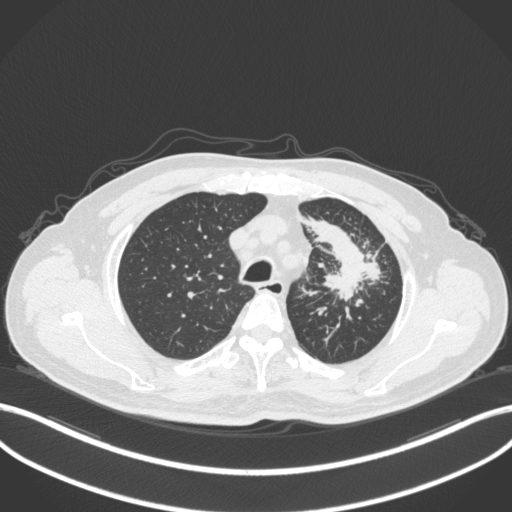
Chest CT, one axial slice; position 281 of 386 along the scan axis; 120 kVp; lung window (W 1500 / L -600 HU); 1 mm slice thickness; 512 × 512 image matrix, field of view 400 × 400 mm. Patient: male, 69 years. Case-level facts recorded for this patient, not image findings: clinical TNM (as recorded): T2a N2 M0; histopathological grade: G2-3.
Outlined on this slice (rectangle marked by the reading radiologist):
- lung tumour (recorded histology: adenocarcinoma): bounding box [x1, y1, x2, y2] px = [306, 212, 390, 307]